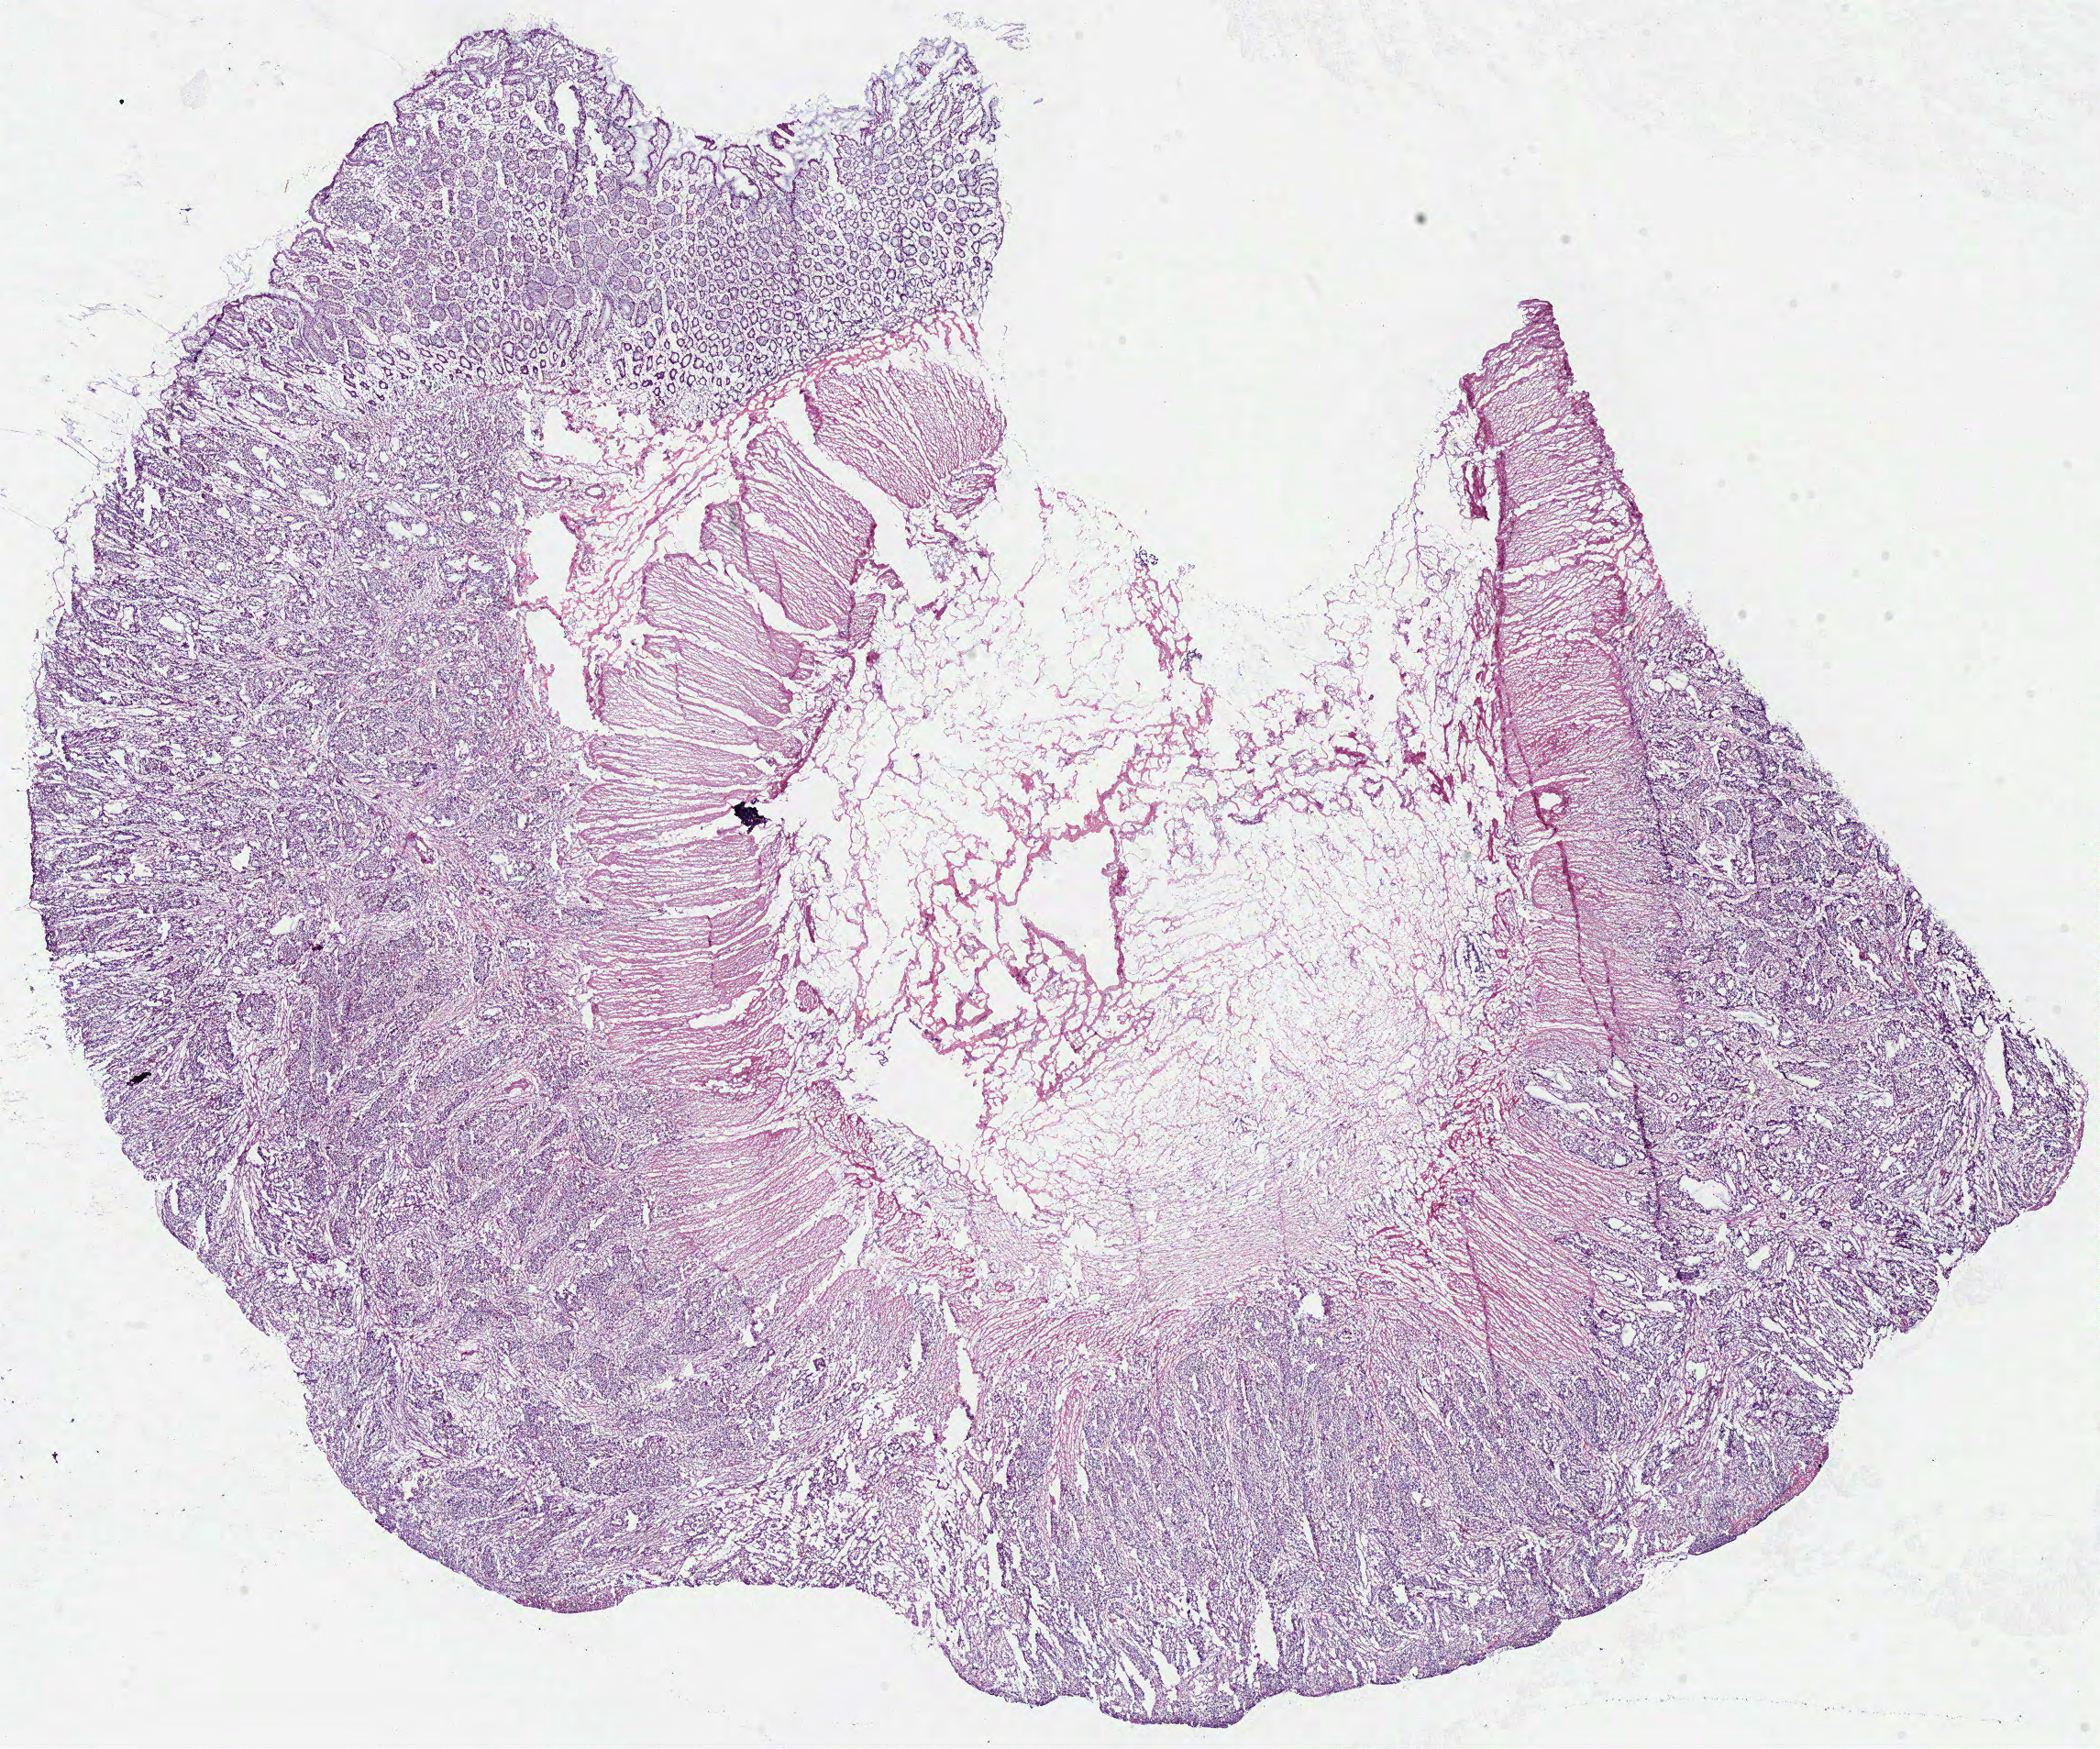
Whole-slide histology image, Hematoxylin and eosin (H&E) stained, a low-resolution overview of the entire scanned area, about 18.0 x 15.0 mm, frozen section from the top of the tissue portion, sample: primary tumour, colon. Female, age 58 years at initial diagnosis. Pathologist review of this section (percent, as recorded): tumour cells 50%, tumour nuclei 75%.
Histologic diagnosis: Adenocarcinoma, NOS.